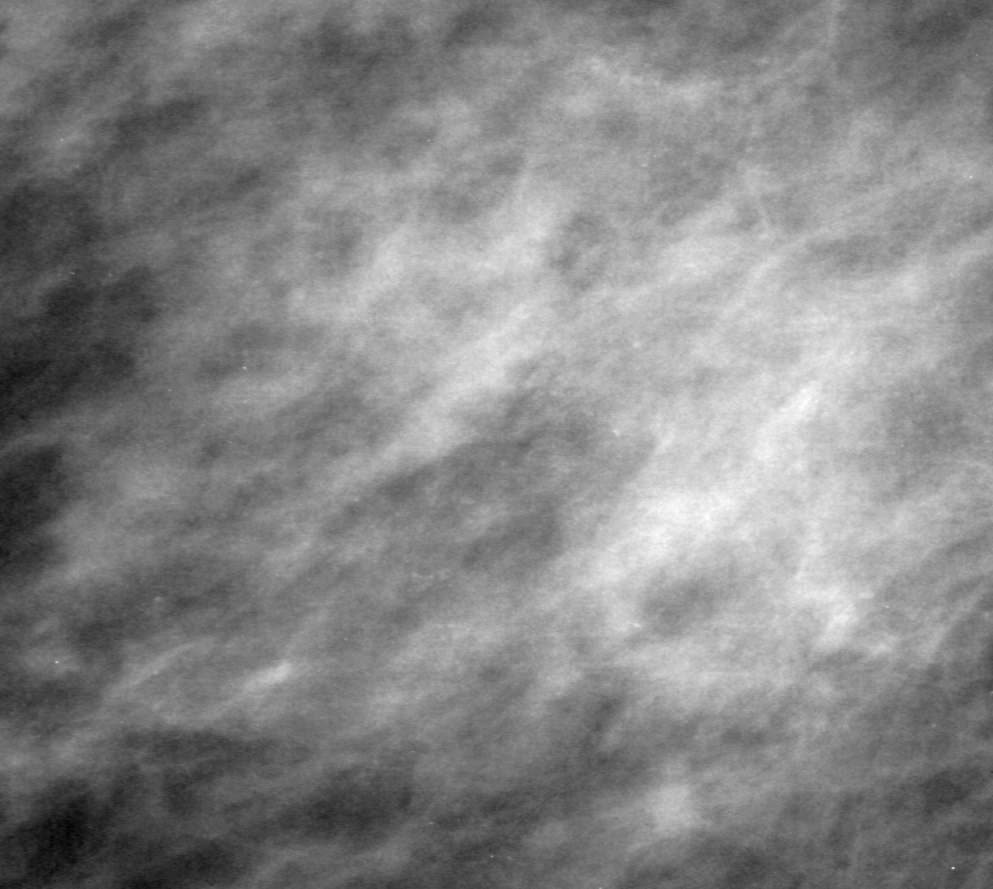
Region of interest cut from a scanned film mammogram (one marked finding); left breast; MLO view; BI-RADS breast density category 3 (scale 1–4).
Finding: calcifications, morphology pleomorphic, distribution segmental; BI-RADS assessment category 4; subtlety rating 2 on a 1 (subtle) to 5 (obvious) scale; pathology result (as recorded, not read from the image): benign.